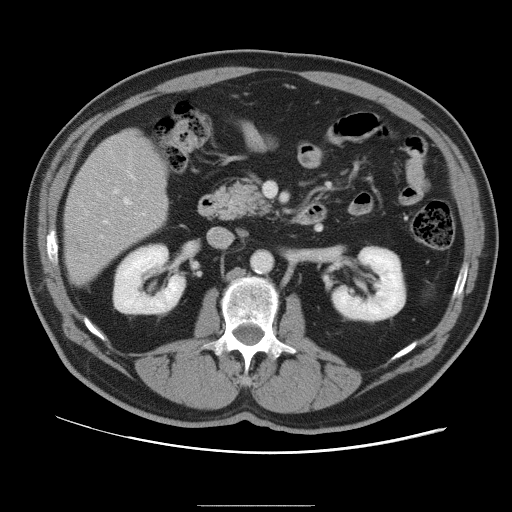
Contrast-enhanced abdominal CT, one axial slice. Soft-tissue window (W 400 / L 40 HU). 5 mm slice thickness. 512 × 512 image matrix. Male patient, age 64 years. Case-level facts recorded for this patient, not image findings: diagnosis: colorectal cancer liver metastases, imaged before liver resection.
Outlined on this slice (manually delineated by an expert):
- hepatic veins: bounding box <104,198,131,223> (left, top, right, bottom; pixels)
- liver: <66,130,168,283>
- planned liver remnant (the part of the liver to remain after resection): <67,130,168,284>
- portal vein (with intrahepatic branches): <101,170,136,238>
- liver metastasis: <68,238,79,249>